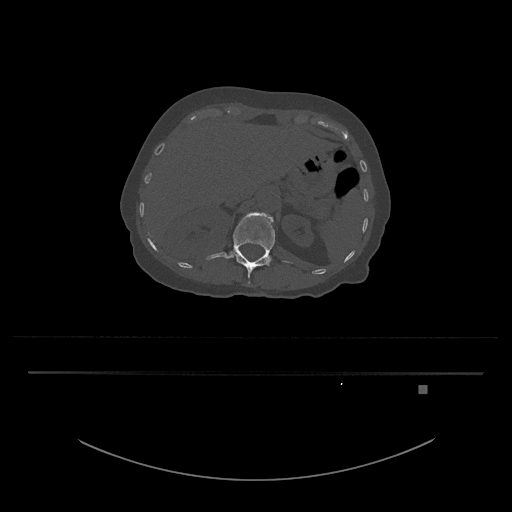
CT including the spine, one axial slice; reconstruction kernel Br40s/3; bone window (W 1800 / L 400 HU); 512 × 512 image matrix, field of view 500 × 500 mm. Female patient, age 57 years. From the clinical record (not read from this slice): primary cancer: cervical.
Outlined on this slice (semi-automatically segmented with operator editing):
- L1 vertebra: bounding box <206,212,289,284> (left, top, right, bottom; pixels)